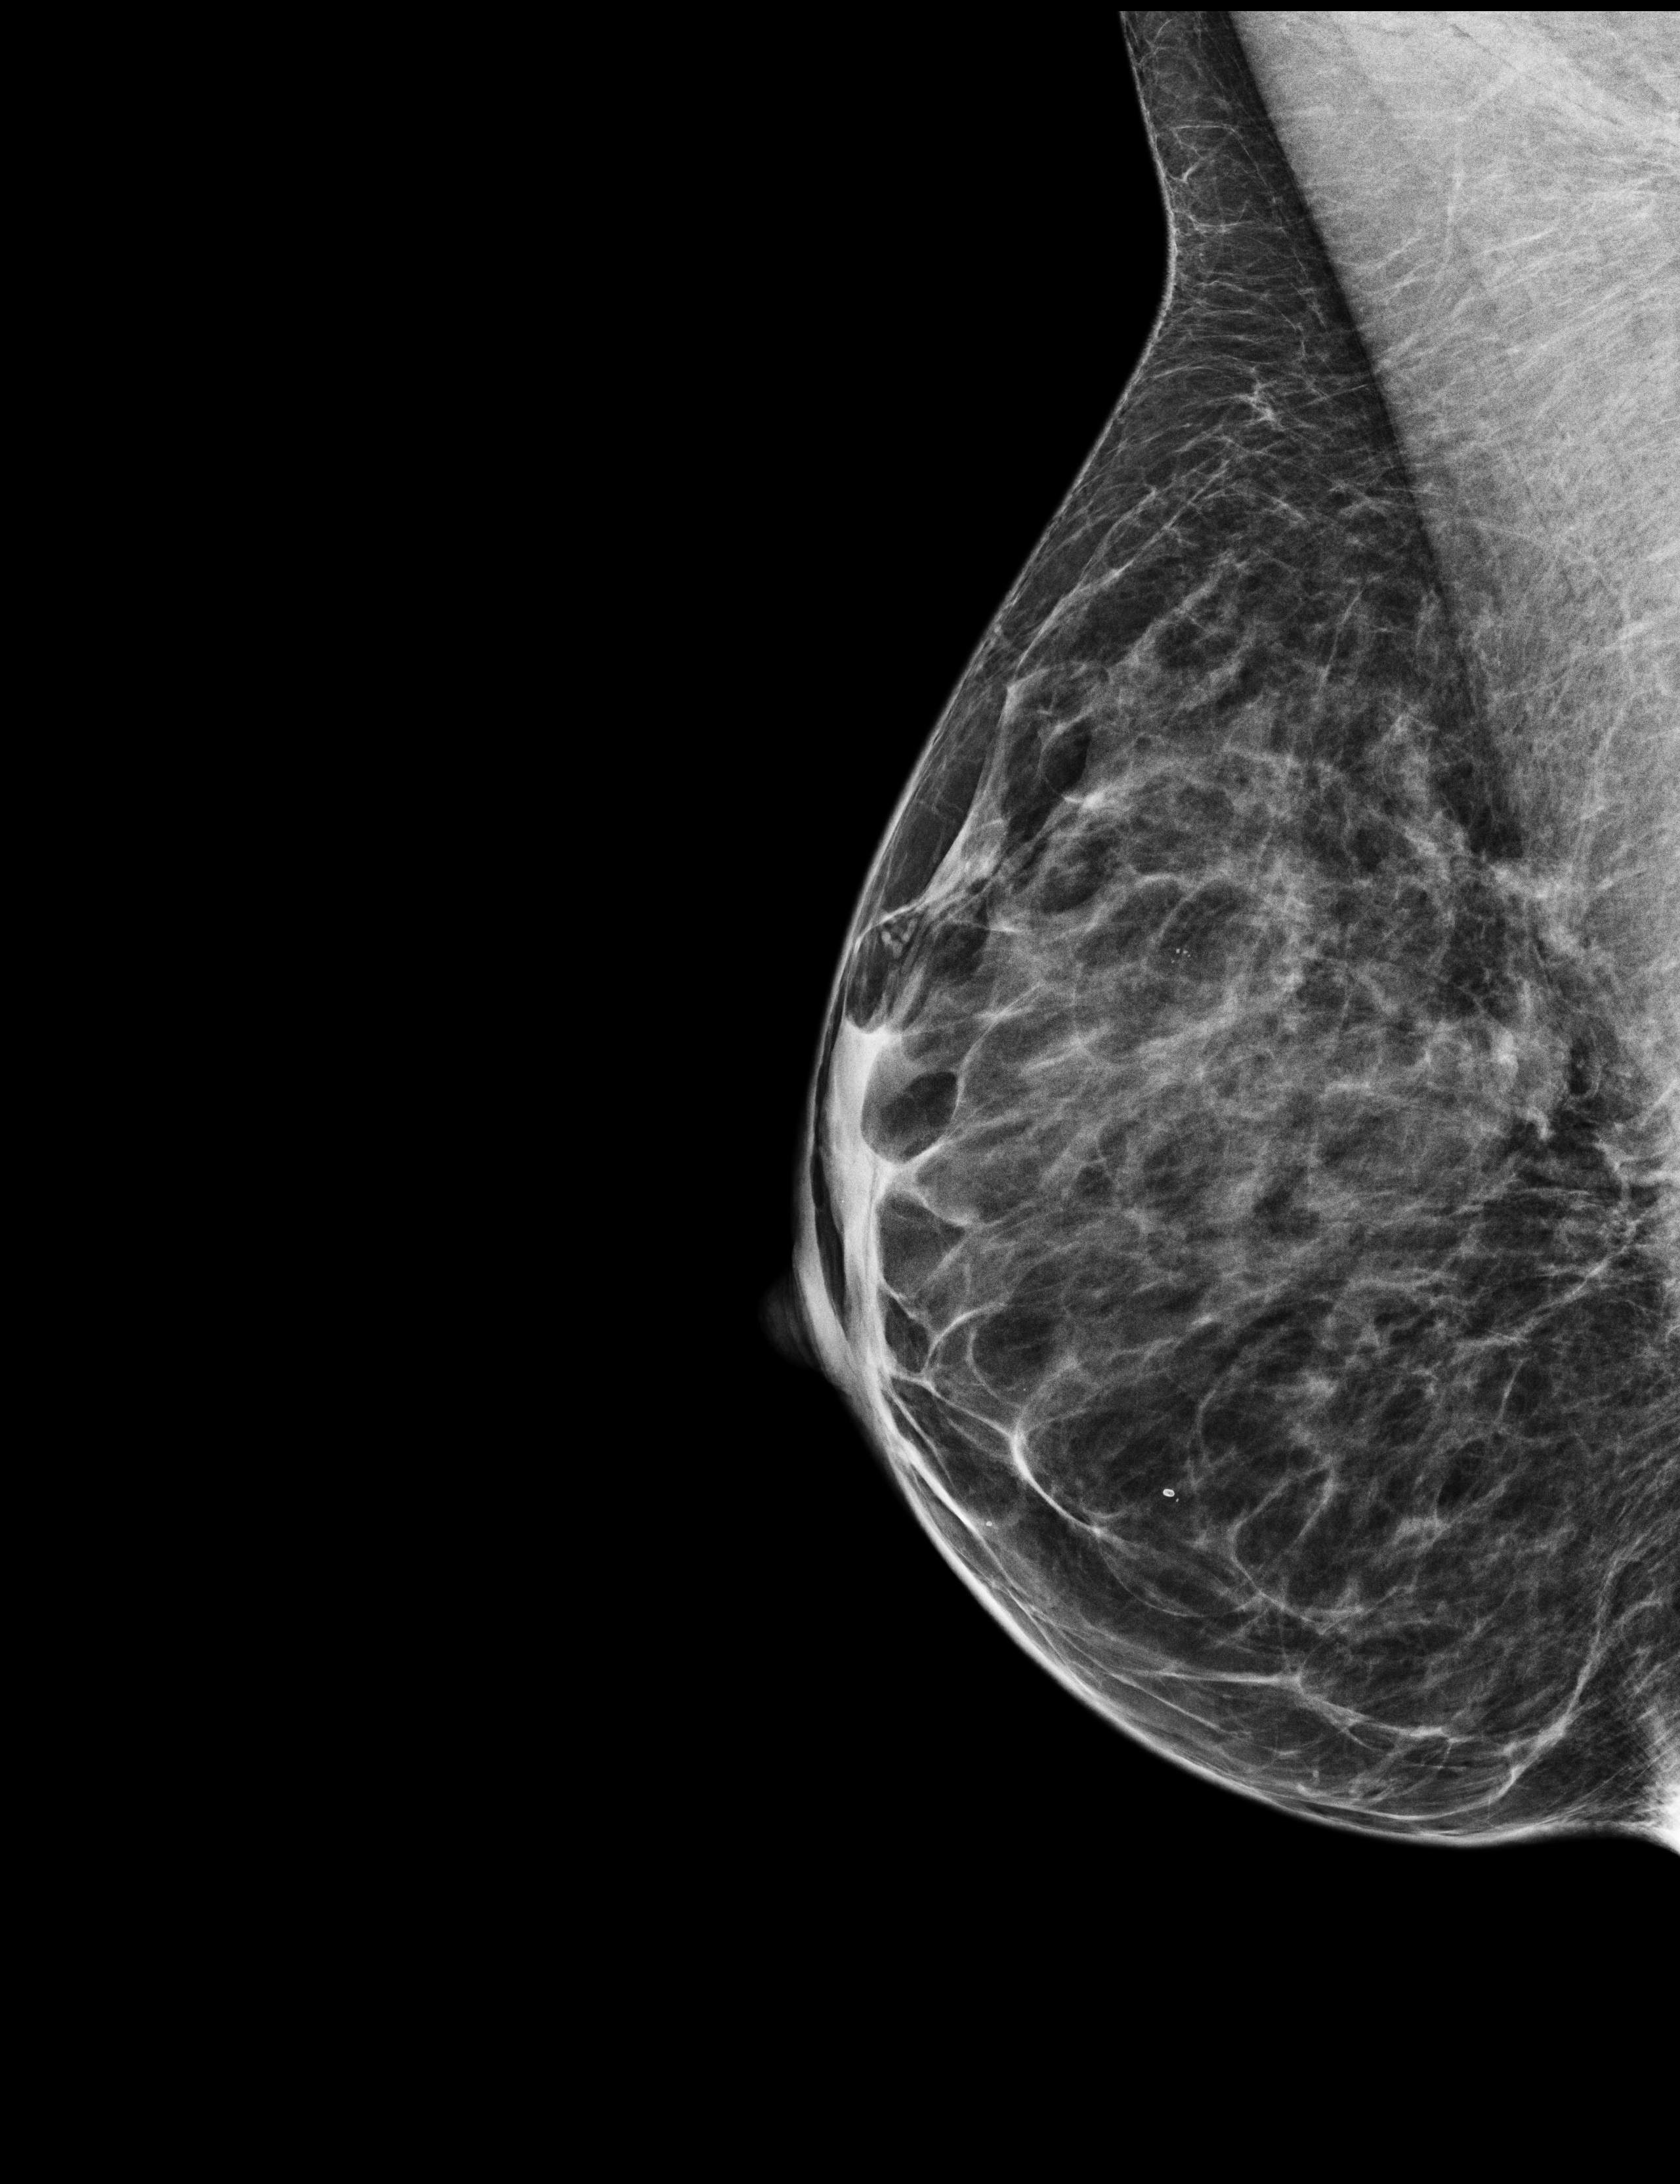
Screening examination, system: Selenia Dimensions. Female patient, age 47 years.
Image type: full-field digital mammogram. Breast: right. Projection: mediolateral oblique (MLO) view.